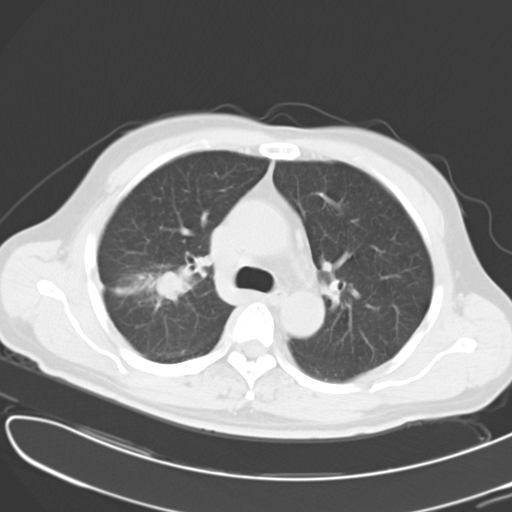
Chest CT, one axial slice. Slice 25 of 37 in the series (ordered by position). 120 kVp. Lung window (W 1500 / L -600 HU). 512 × 512 image matrix, field of view 353 × 353 mm. Patient: male, 53 years. Case-level facts recorded for this patient, not image findings: clinical TNM (as recorded): T2 N1 M0.
Outlined on this slice (bounding box drawn by a radiologist):
- lung tumour (recorded histology: adenocarcinoma): bounding box (x1, y1, x2, y2) in pixels: (105, 262, 194, 307)